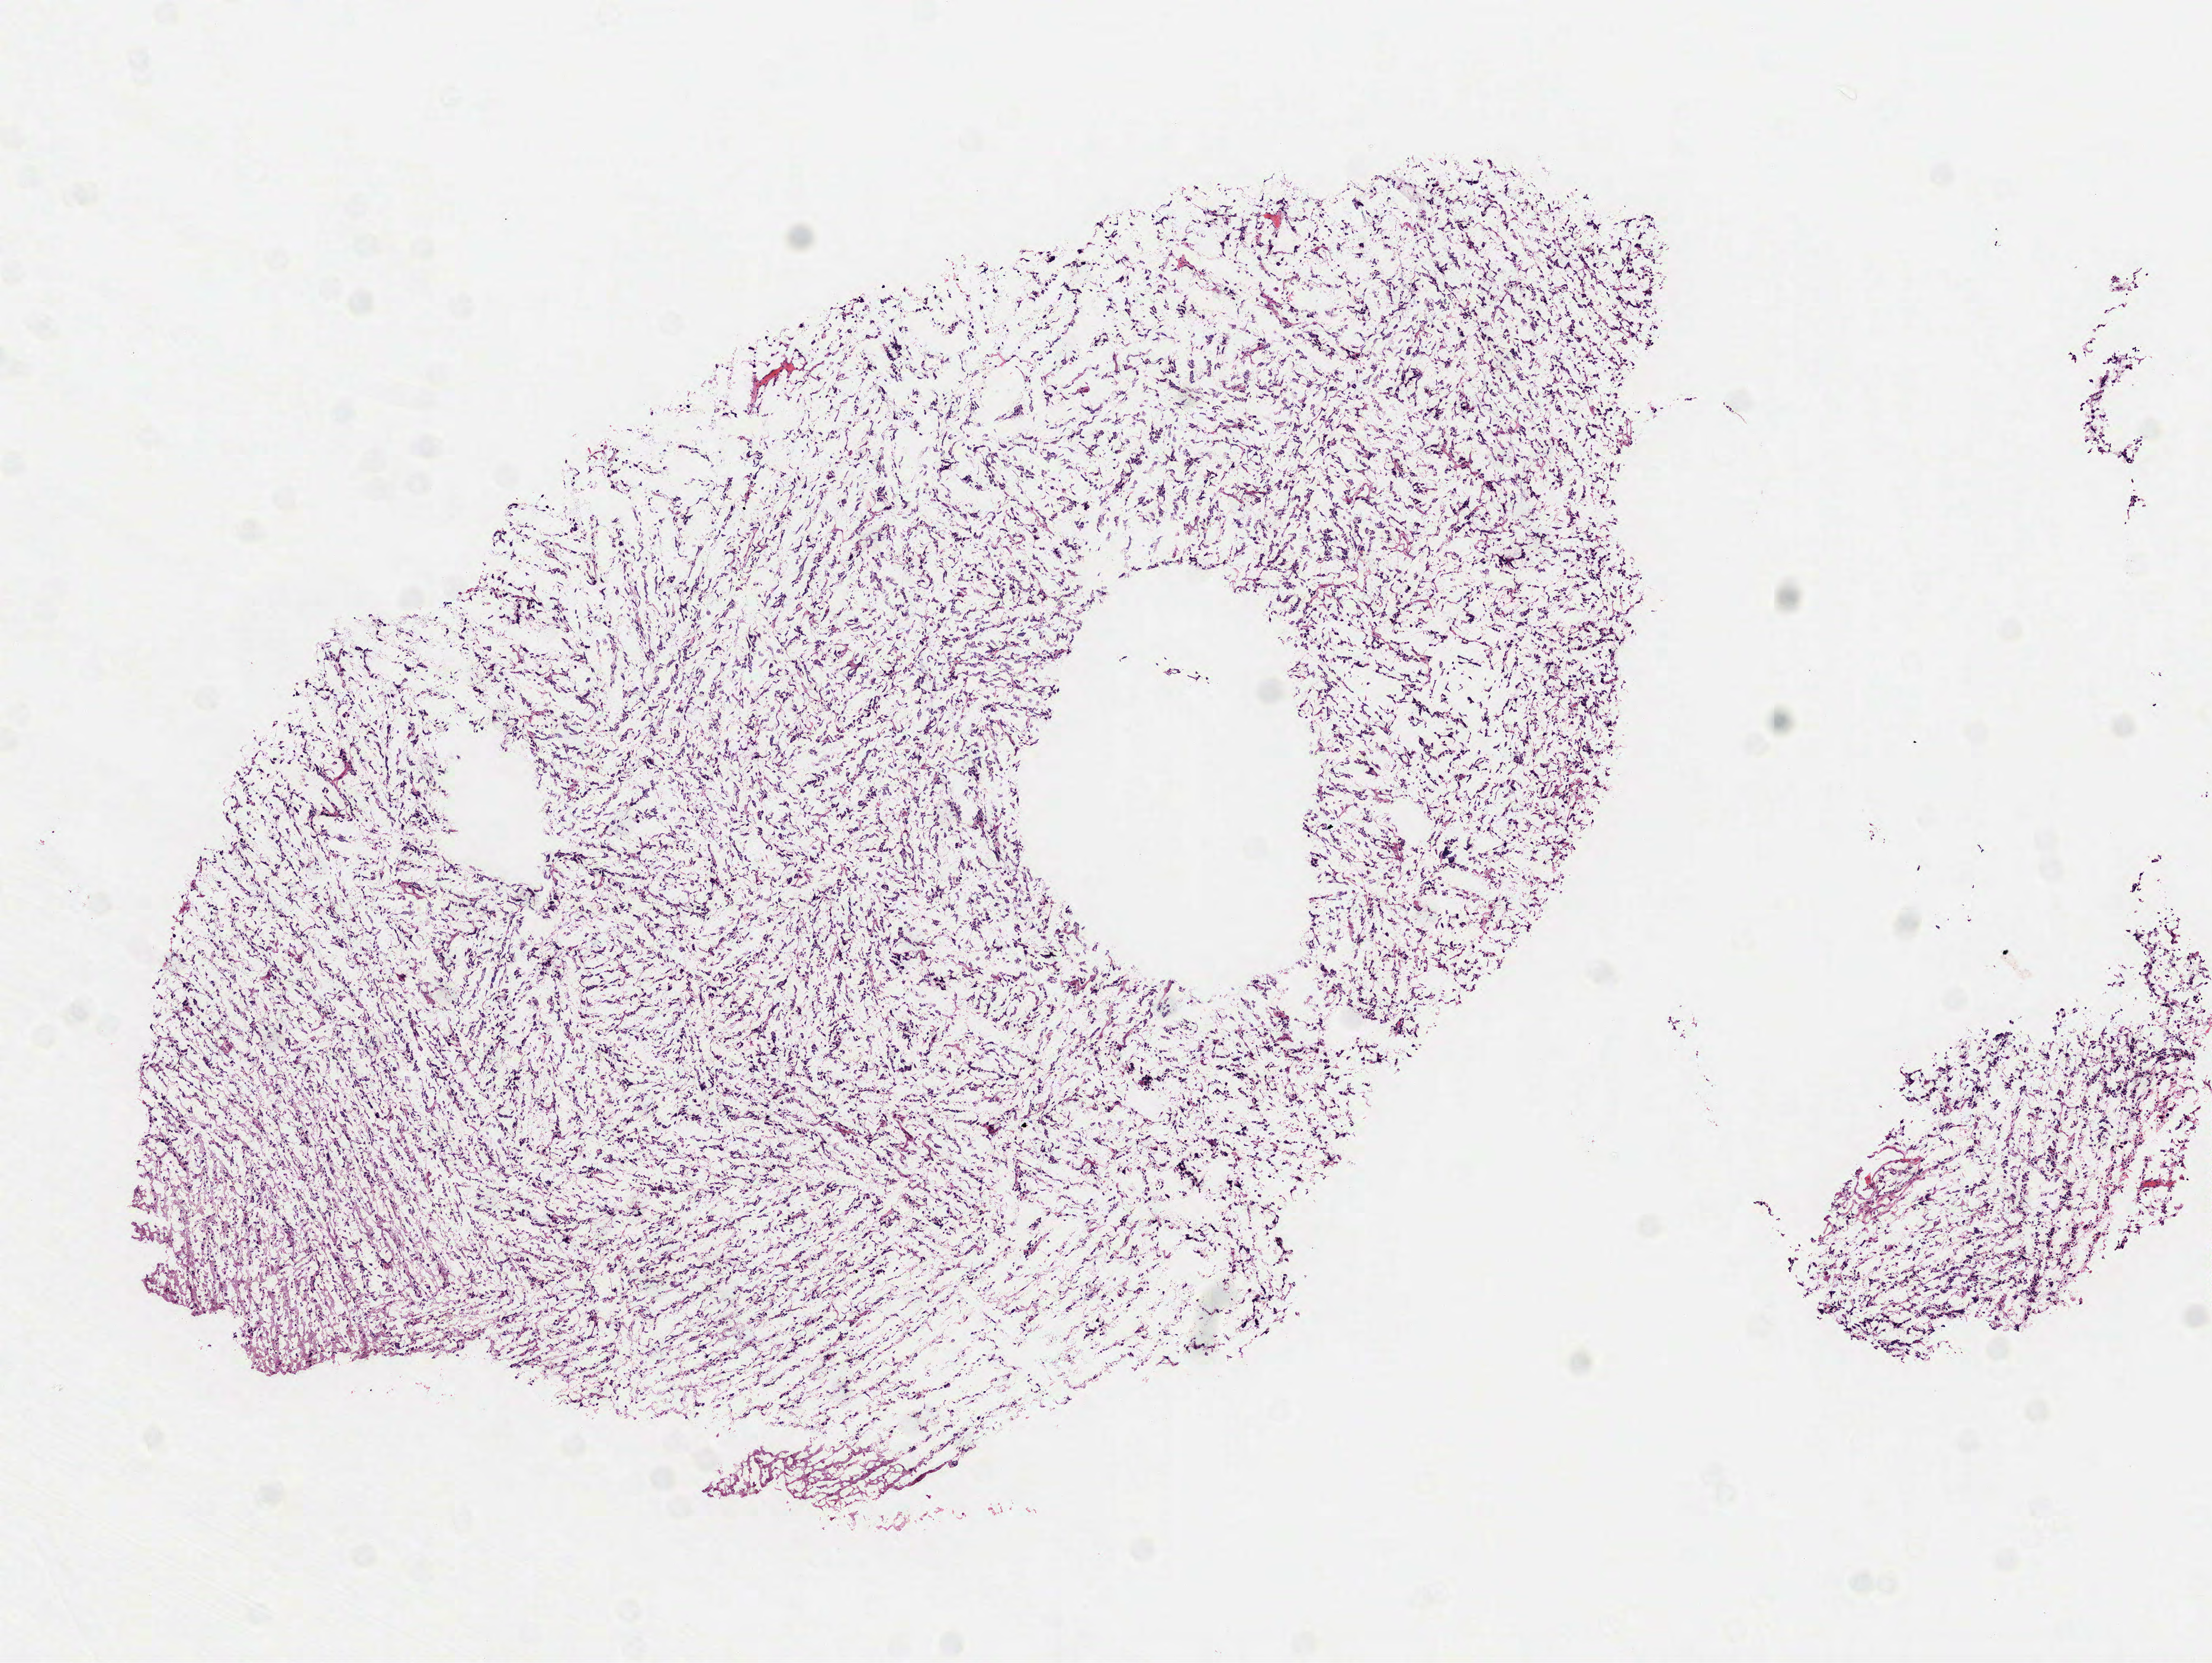
H&E whole-slide image — a low-resolution overview of the entire scanned area, about 7.5 x 5.7 mm (acquisition: 40x scan). Frozen section from the top of the tissue portion. Brain, primary tumour sample. Female patient; age at initial diagnosis 53 years. Slide review estimates, as recorded: tumour cells 100%, tumour nuclei 80%, normal cells 0%, stromal cells 0%, necrosis 0%.
Diagnosis: Glioblastoma.